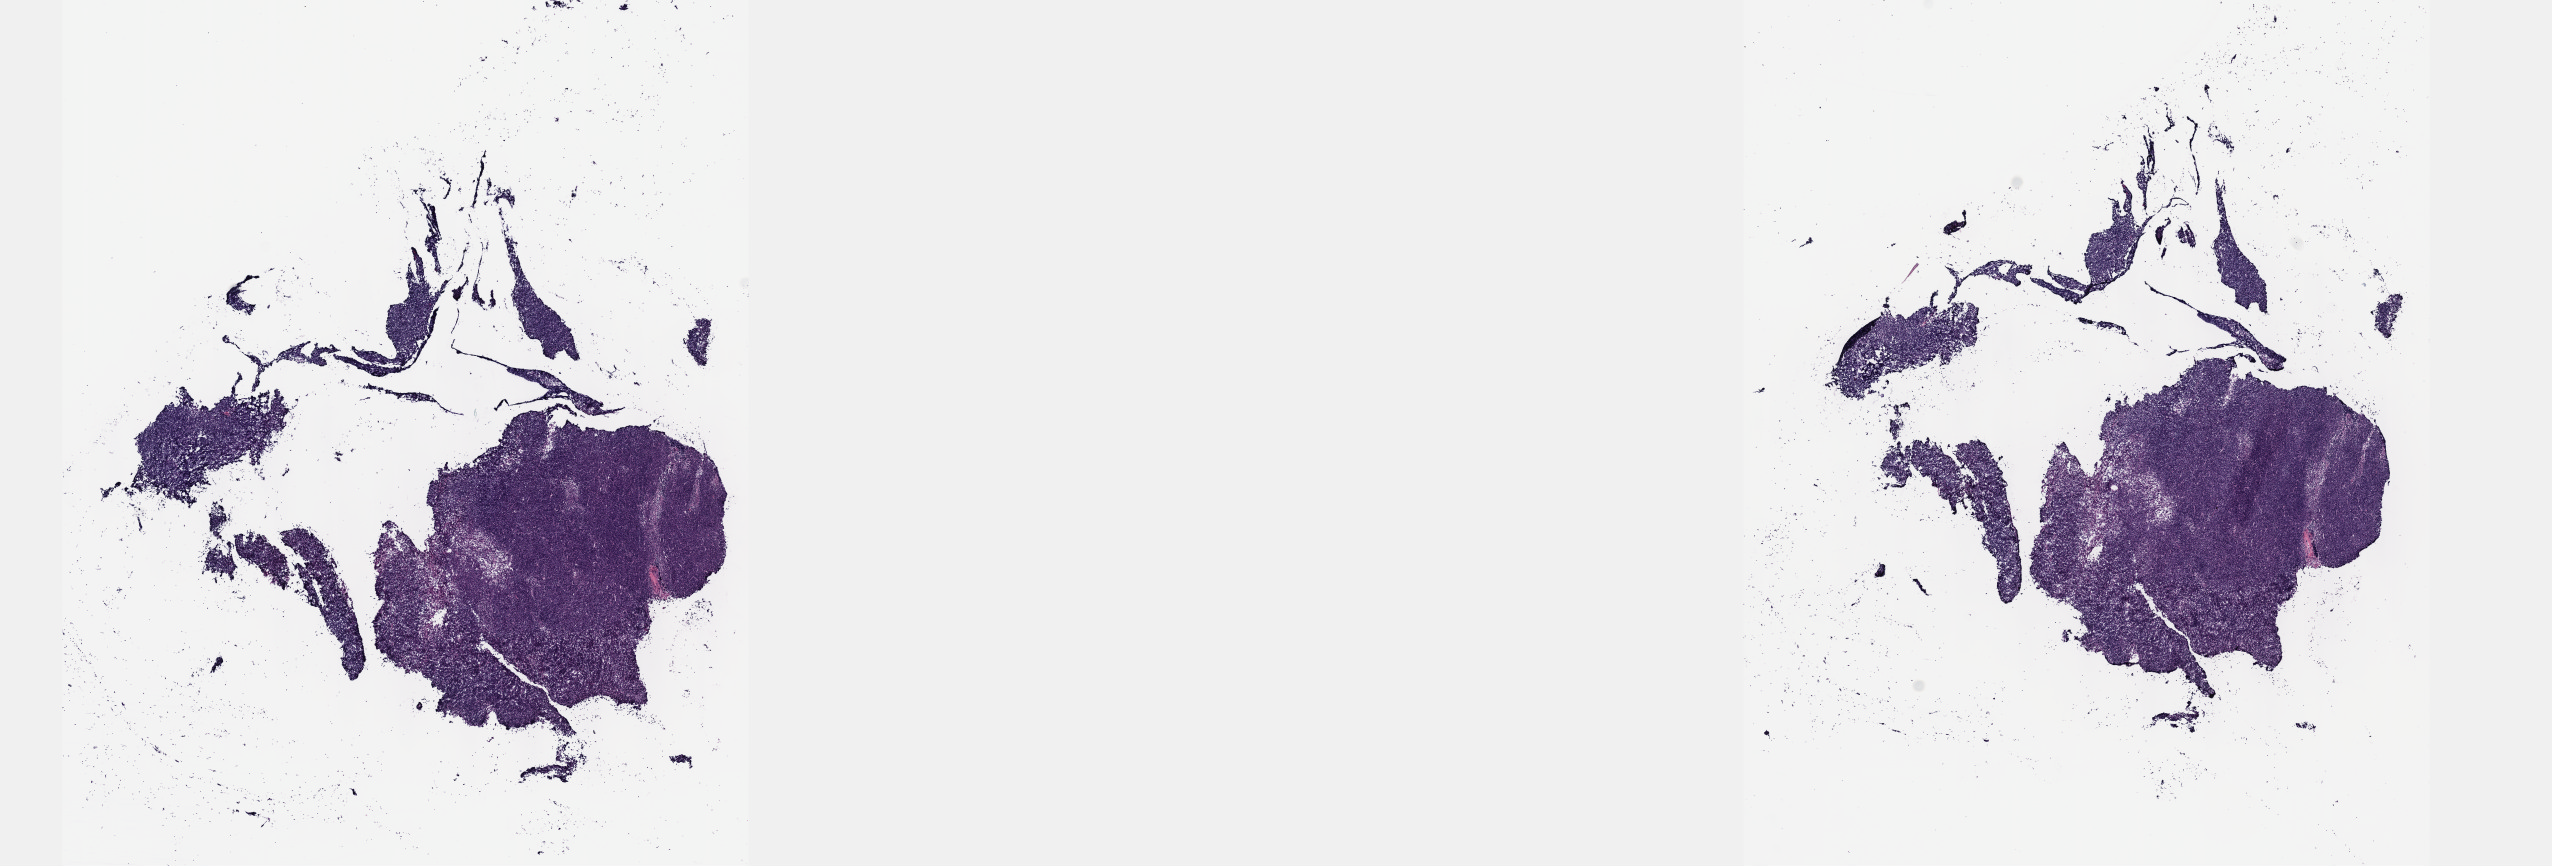
Digitized H&E-stained tissue section (whole slide), a low-resolution overview of the entire scanned area, about 20.6 x 7.0 mm (from a 40x scan). Frozen section from the top of the tissue portion. Thymus, primary tumour sample. Male, age 68 years at initial diagnosis. Slide review estimates, as recorded: tumour cells 99%, tumour nuclei 99%, normal cells 0%, stromal cells 1%, necrosis 0%. Inflammatory infiltration, as recorded: lymphocyte infiltration 0%, monocyte infiltration 0%, neutrophil infiltration 0%.
Histologic diagnosis: Thymoma, type AB, malignant.